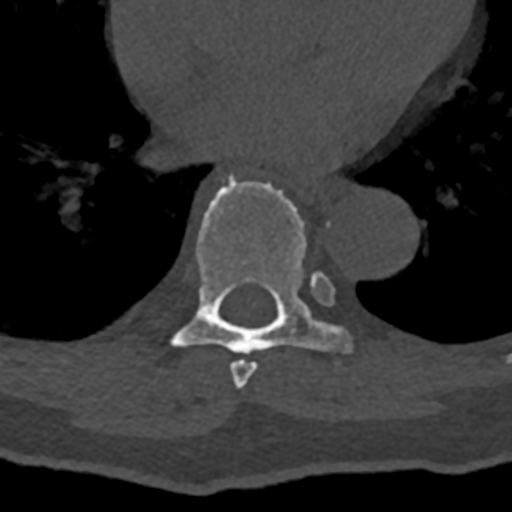
CT including the spine, one axial slice; position 716 of 797 along the scan axis; bone window (W 1800 / L 400 HU); 0.5 mm slice thickness; 512 × 512 image matrix. Patient: male, 74 years. From the clinical record (not read from this slice): primary cancer: renal; vertebrae with lytic lesions (as recorded): T10, L1, L2, L3, L4, L5.
Annotated regions visible in this slice (semi-automatically segmented with operator editing):
- T7 vertebra: bounding box (x1, y1, x2, y2) in pixels: (230, 273, 332, 389)
- T8 vertebra: (164, 170, 351, 355)